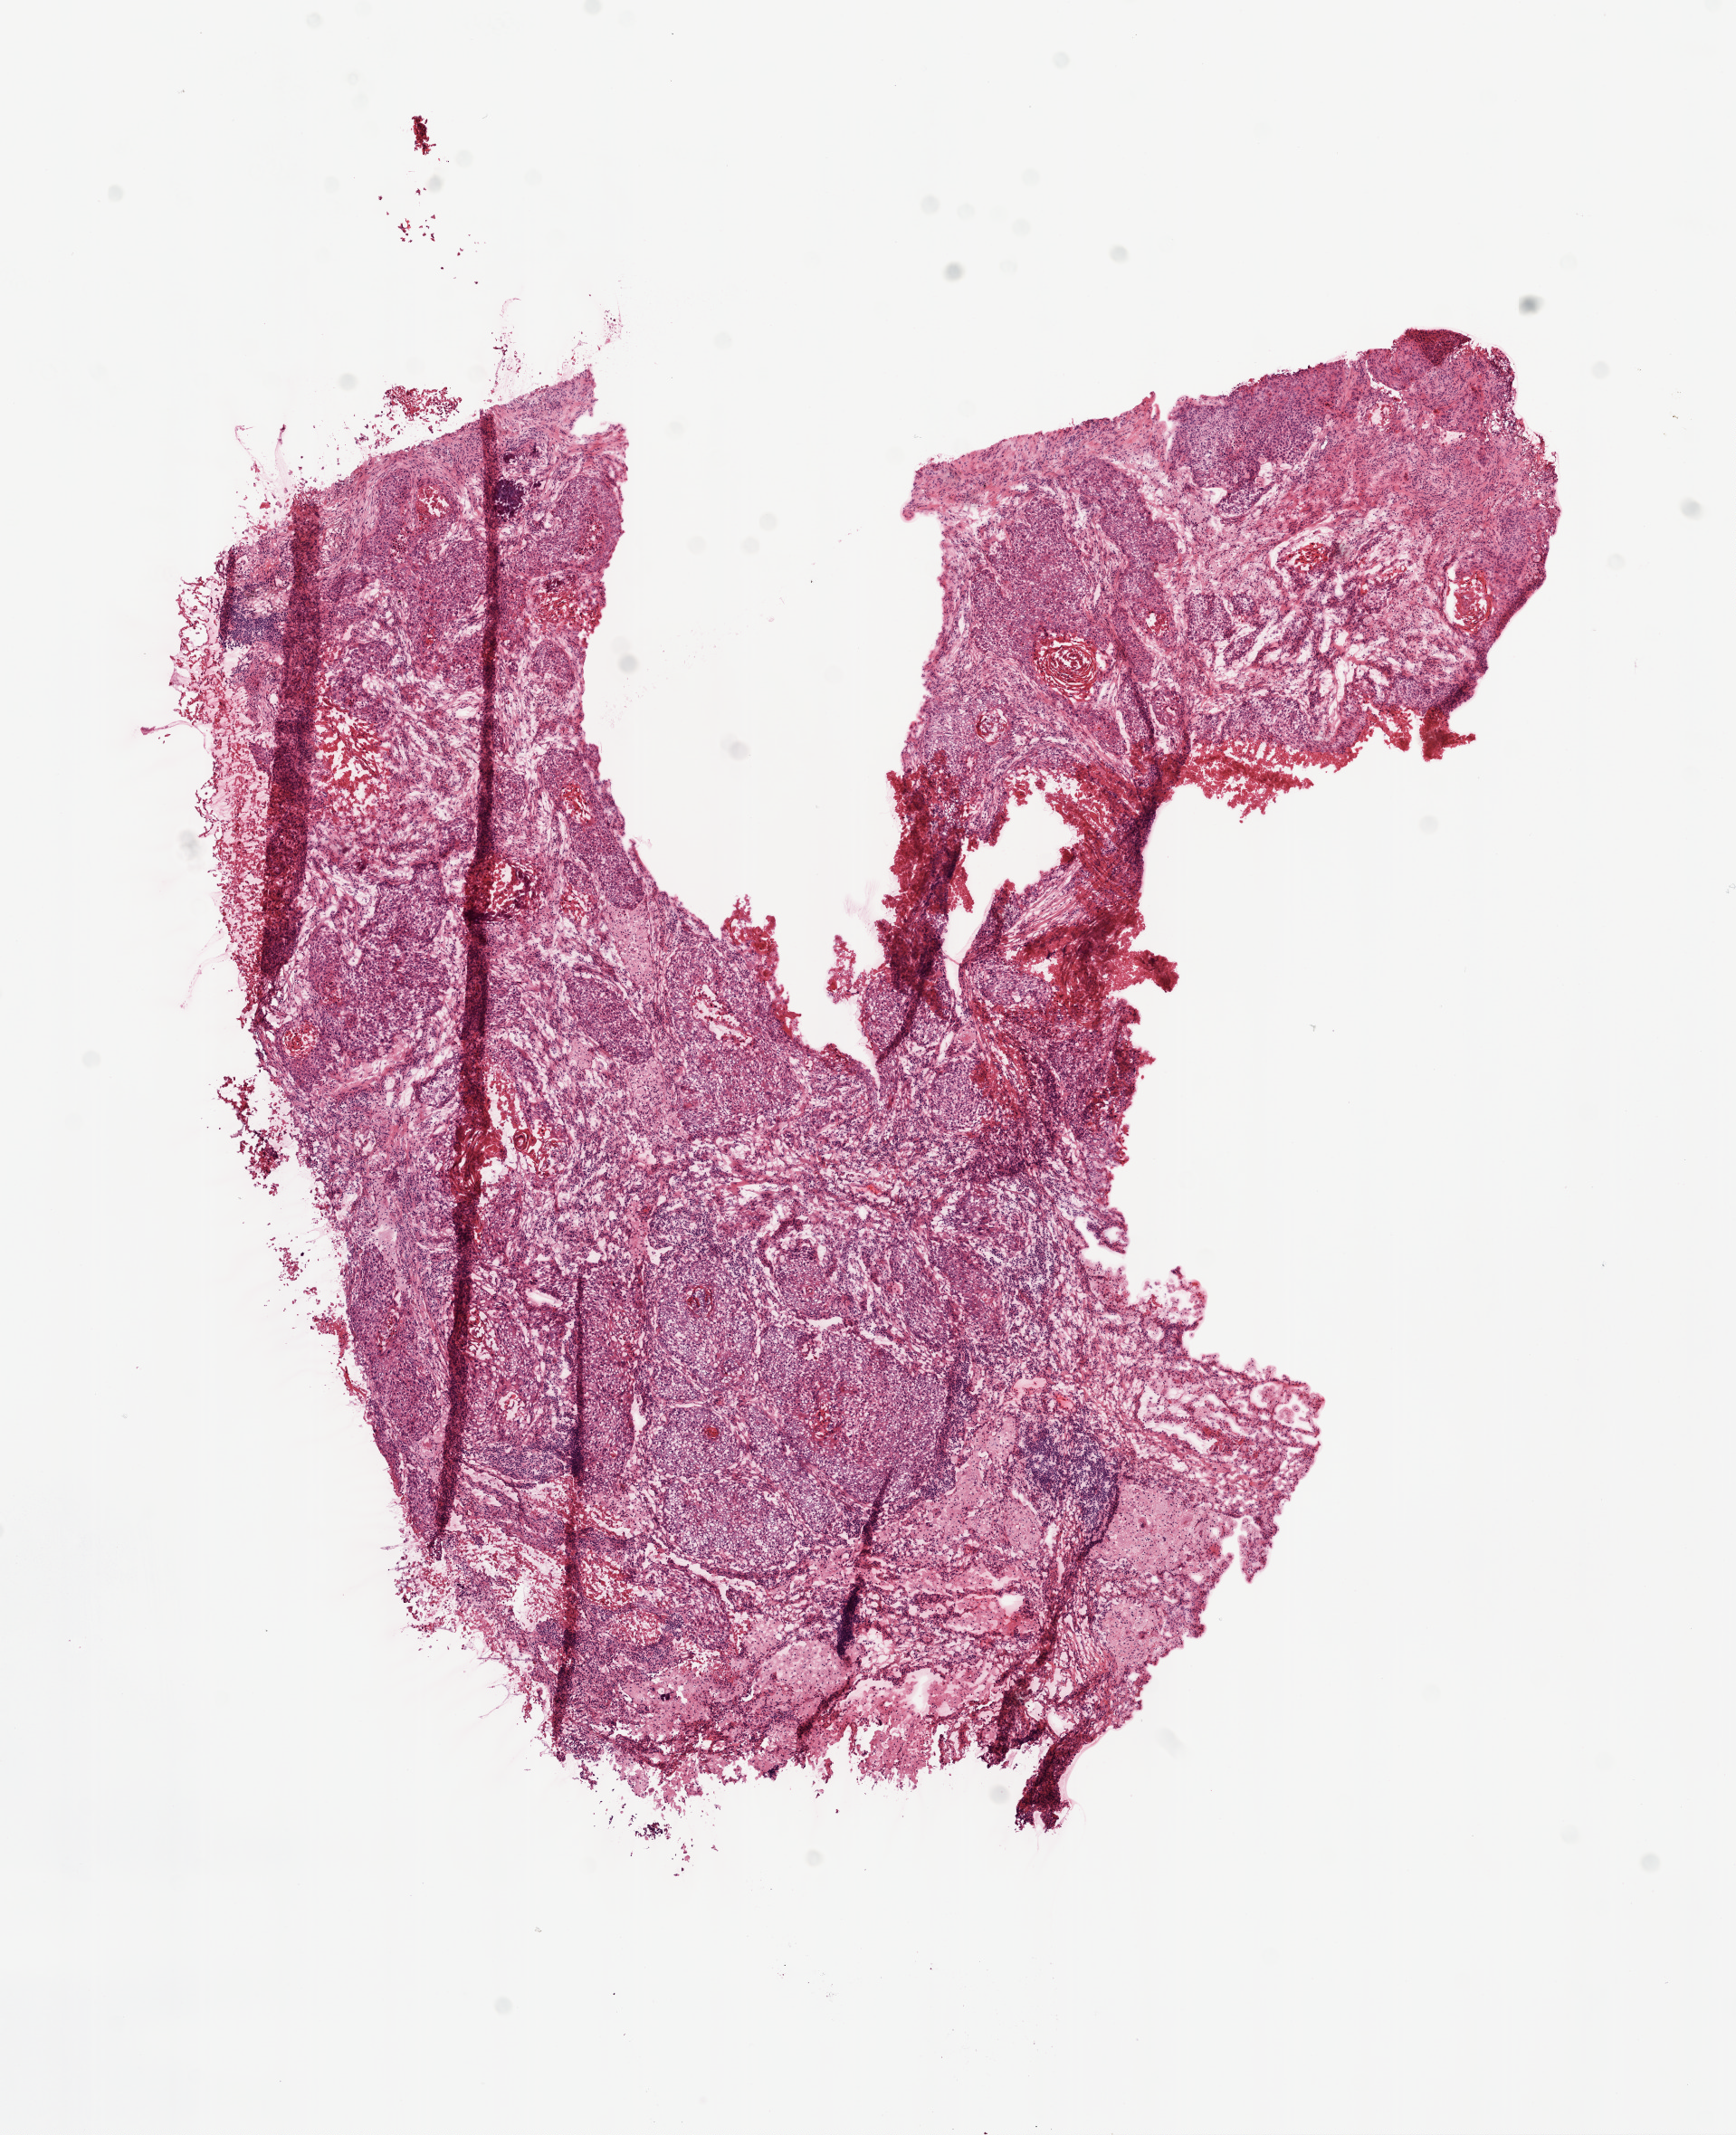
Whole-slide histology image, Hematoxylin and eosin (H&E) stained — shown as a low-resolution overview of the whole scanned area (about 7.7 x 9.5 mm, slide scanned at 20x); frozen section from the top of the tissue portion; sample: primary tumour, lung. Female, age 54 years at initial diagnosis.
TNM: T2 N0 M0. Diagnosis: Squamous cell carcinoma, NOS. AJCC pathologic stage: IB.